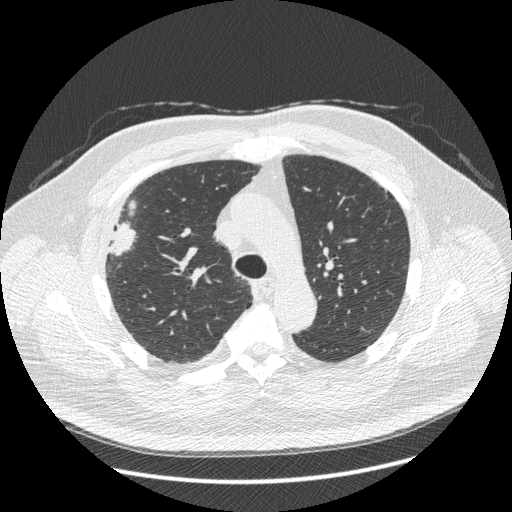
Chest CT (low-dose screening protocol), one axial image, third annual screen, lung window (W 1500 / L -600 HU), 1.25 mm slice thickness, slice 123 of 426 in the series. Male participant, aged 66 years at enrolment. Current smoker at enrolment.
Expert reader's lesion annotation, bounding box <87,203,147,269> (left, top, right, bottom; pixels). The exam's reader record, not a measurement of the box and not confirmed to be the same lesion: non-calcified nodule or mass ≥4 mm, right upper lobe, 48 × 25 mm, spiculated (stellate) margins, soft tissue attenuation, pre-existing on the prior screen: no. Official screen result: positive, other. Participant outcome: lung cancer diagnosed 35 days after this screen — non-small cell carcinoma, right upper lobe, stage IV (AJCC 6th edition), 50 mm at pathology.